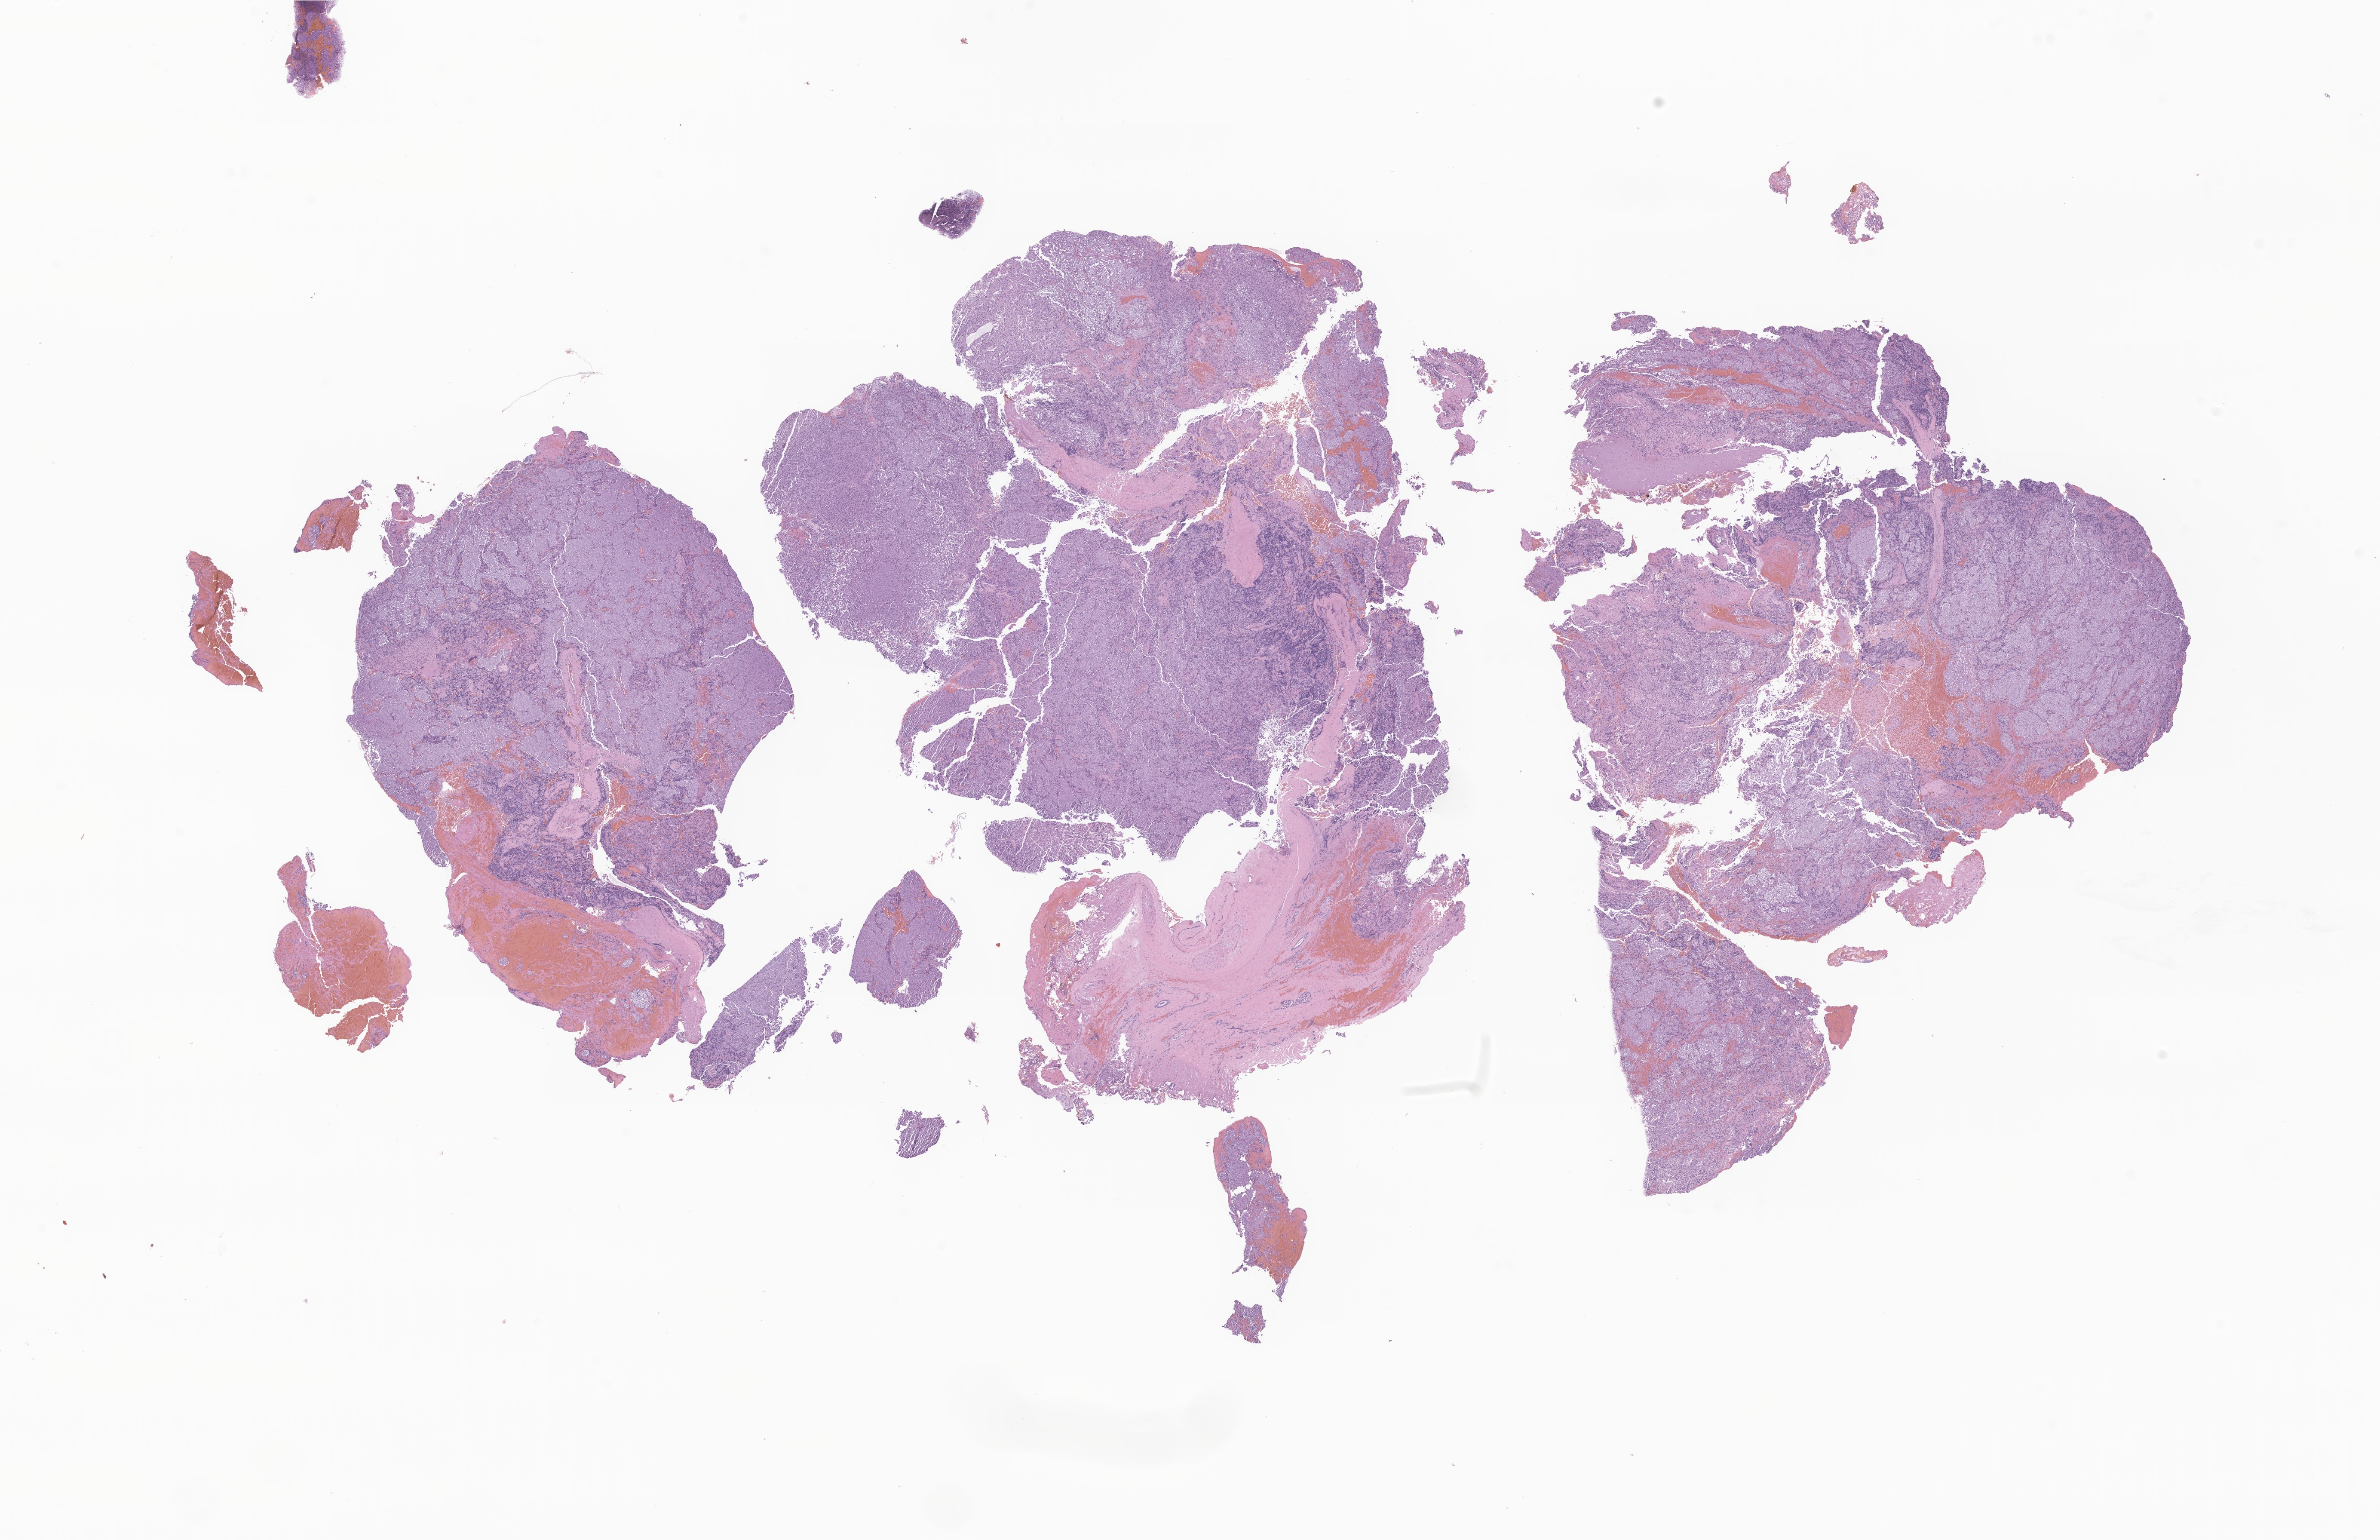
Haematoxylin and eosin whole-slide image of tumor tissue from the peritoneum — a low-resolution overview of the entire scanned area, about 23.3 x 15.1 mm. Formalin-fixed paraffin-embedded section. Patient: female, age 86 months (7 years 2 months).
* recorded diagnosis: Pancreatoblastoma